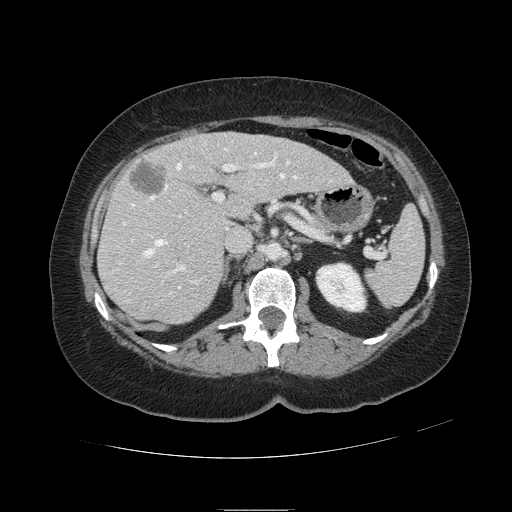
Contrast-enhanced abdominal CT, one axial slice. Position 62 of 121 along the scan axis. 120 kVp. Intravenous contrast given. Soft-tissue window (W 400 / L 40 HU). 2.5 mm slice thickness. 512 × 512 image matrix, field of view 400 × 400 mm. Female patient, age 52 years. Case-level facts recorded for this patient, not image findings: diagnosis: colorectal cancer liver metastases, imaged before liver resection; multiple liver metastases: yes; largest metastasis: 6.3 cm; chemotherapy before resection: yes.
Structures marked on this image (outlined manually by an expert reader):
- hepatic veins: bounding box [x1, y1, x2, y2] px = [119, 148, 333, 295]
- liver: [99, 133, 351, 324]
- planned liver remnant (the part of the liver to remain after resection): [167, 133, 352, 219]
- portal vein (with intrahepatic branches): [123, 153, 277, 273]
- liver metastasis: [130, 164, 166, 196]